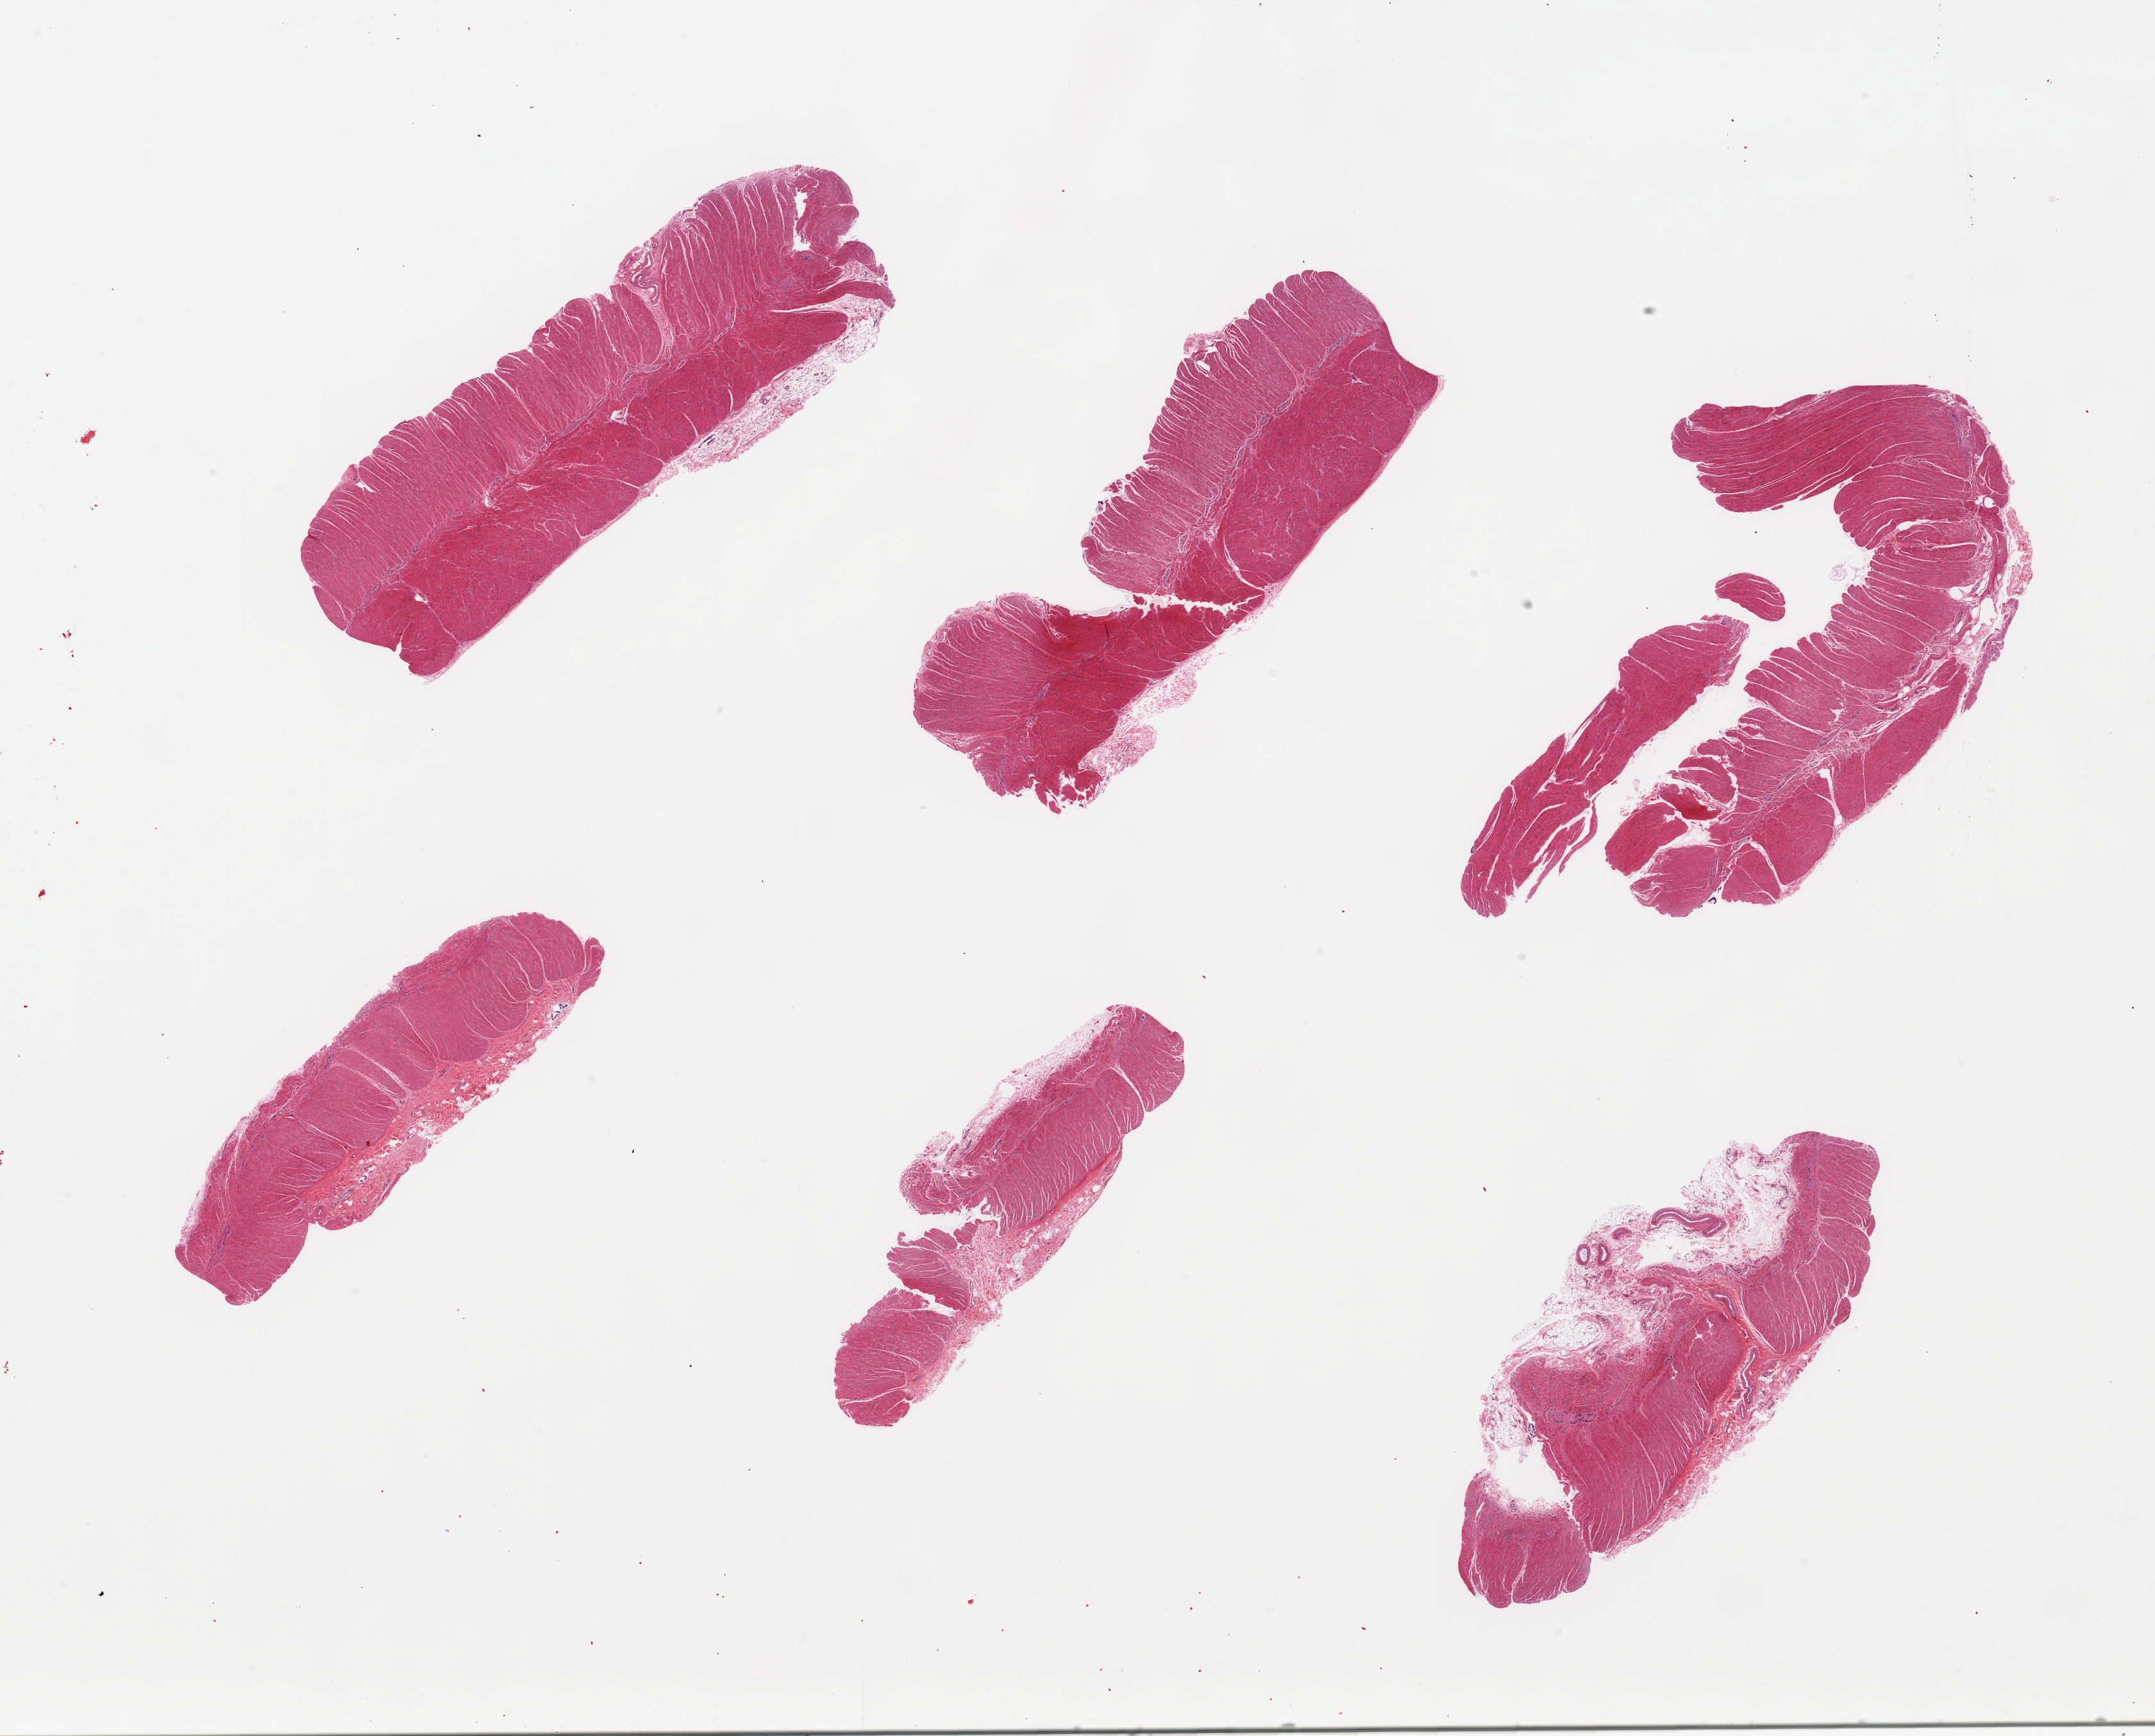
Whole-slide image, hematoxylin and eosin (H&E) stain, a low-resolution overview of the entire scanned area, about 26.6 x 21.4 mm (from a 20x scan); PAXgene-fixed, paraffin-embedded tissue; section of sigmoid colon (target tissue); tissue donor sample. Donor sex: male.
* reviewer comment on this tissue sample: 6 pieces, confirmed target muscularis